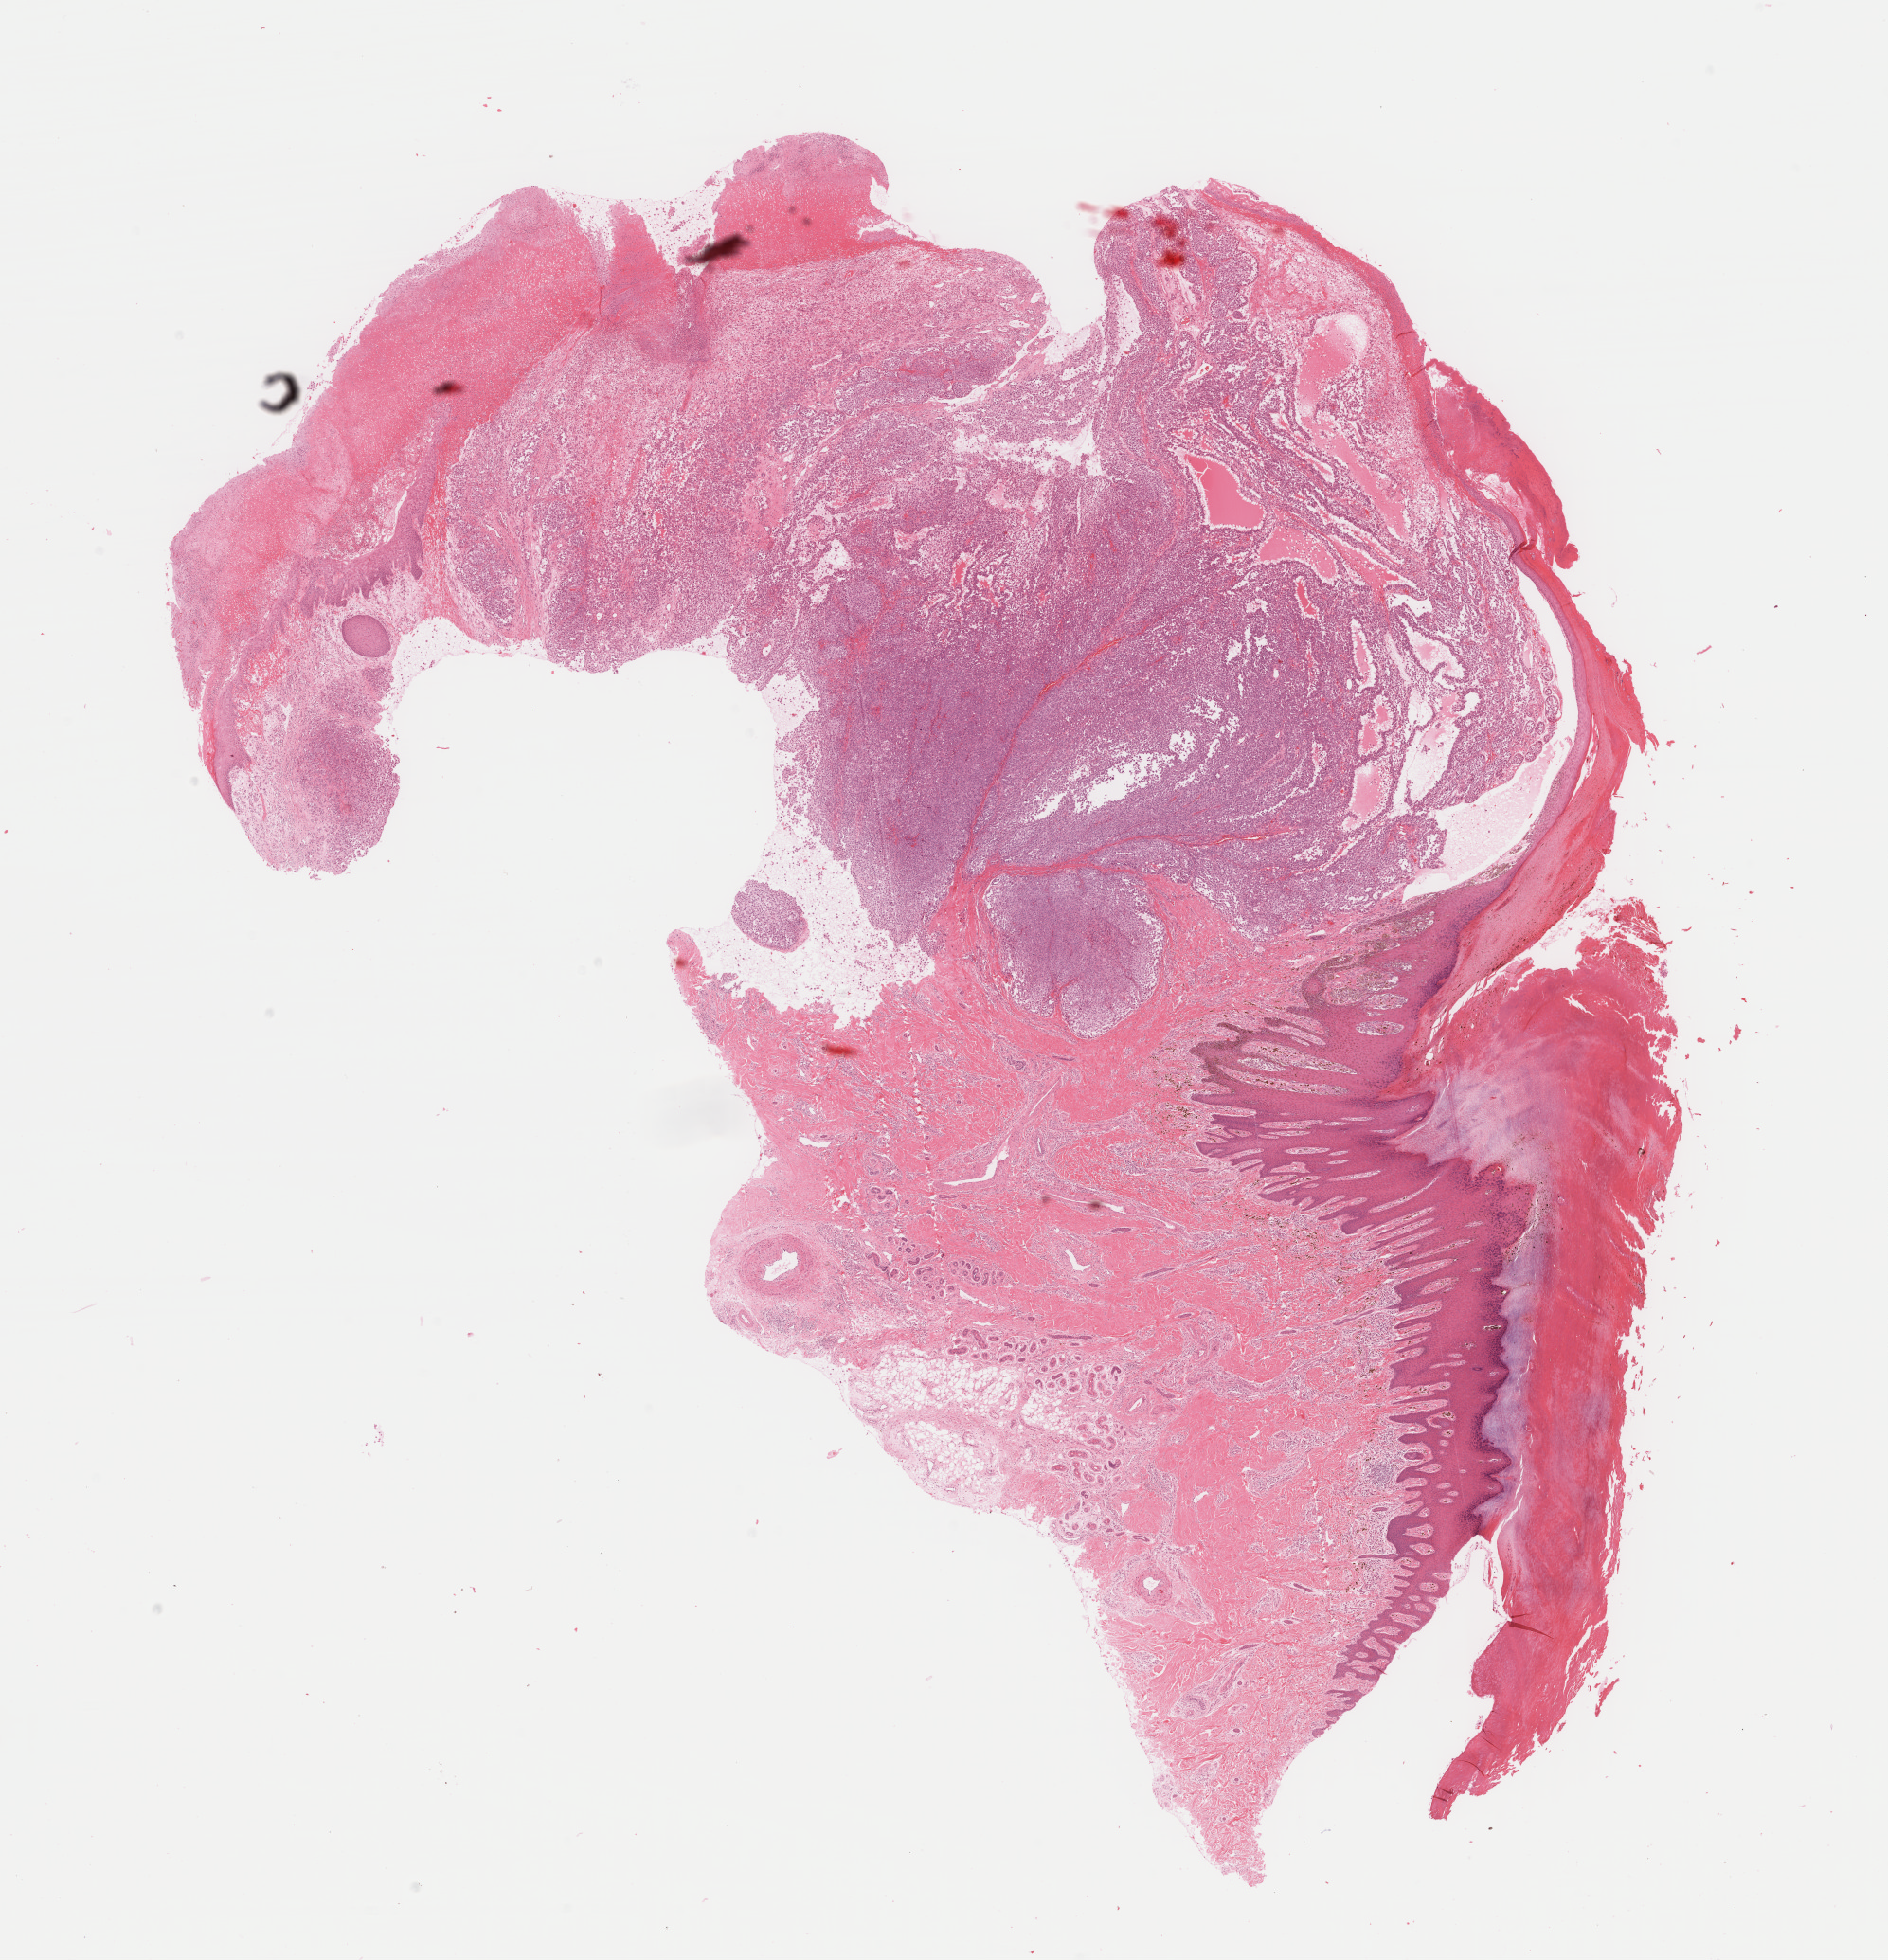
Whole-slide histology image, H&E — shown as a low-resolution overview of the whole scanned area (about 15.8 x 16.4 mm, acquisition: 40x scan); formalin-fixed paraffin-embedded (FFPE) diagnostic section; sample: primary tumour, skin. Male, age 56 years at initial diagnosis.
Pathologic diagnosis: Malignant melanoma, NOS.